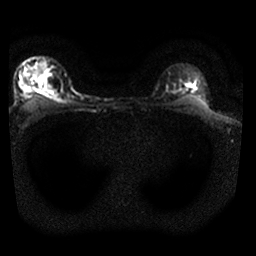
Breast MRI, one axial slice. Diffusion-weighted series; image 2 of 4 stored at this slice position (different b-values; order by instance number). 1.5 T. 4 mm slice thickness. 256 × 256 image matrix, field of view 310 × 310 mm. Female patient.
Structures marked on this image (manually delineated by an expert):
- tumour on diffusion-weighted imaging: bounding box [x1, y1, x2, y2] px = [38, 80, 50, 94]